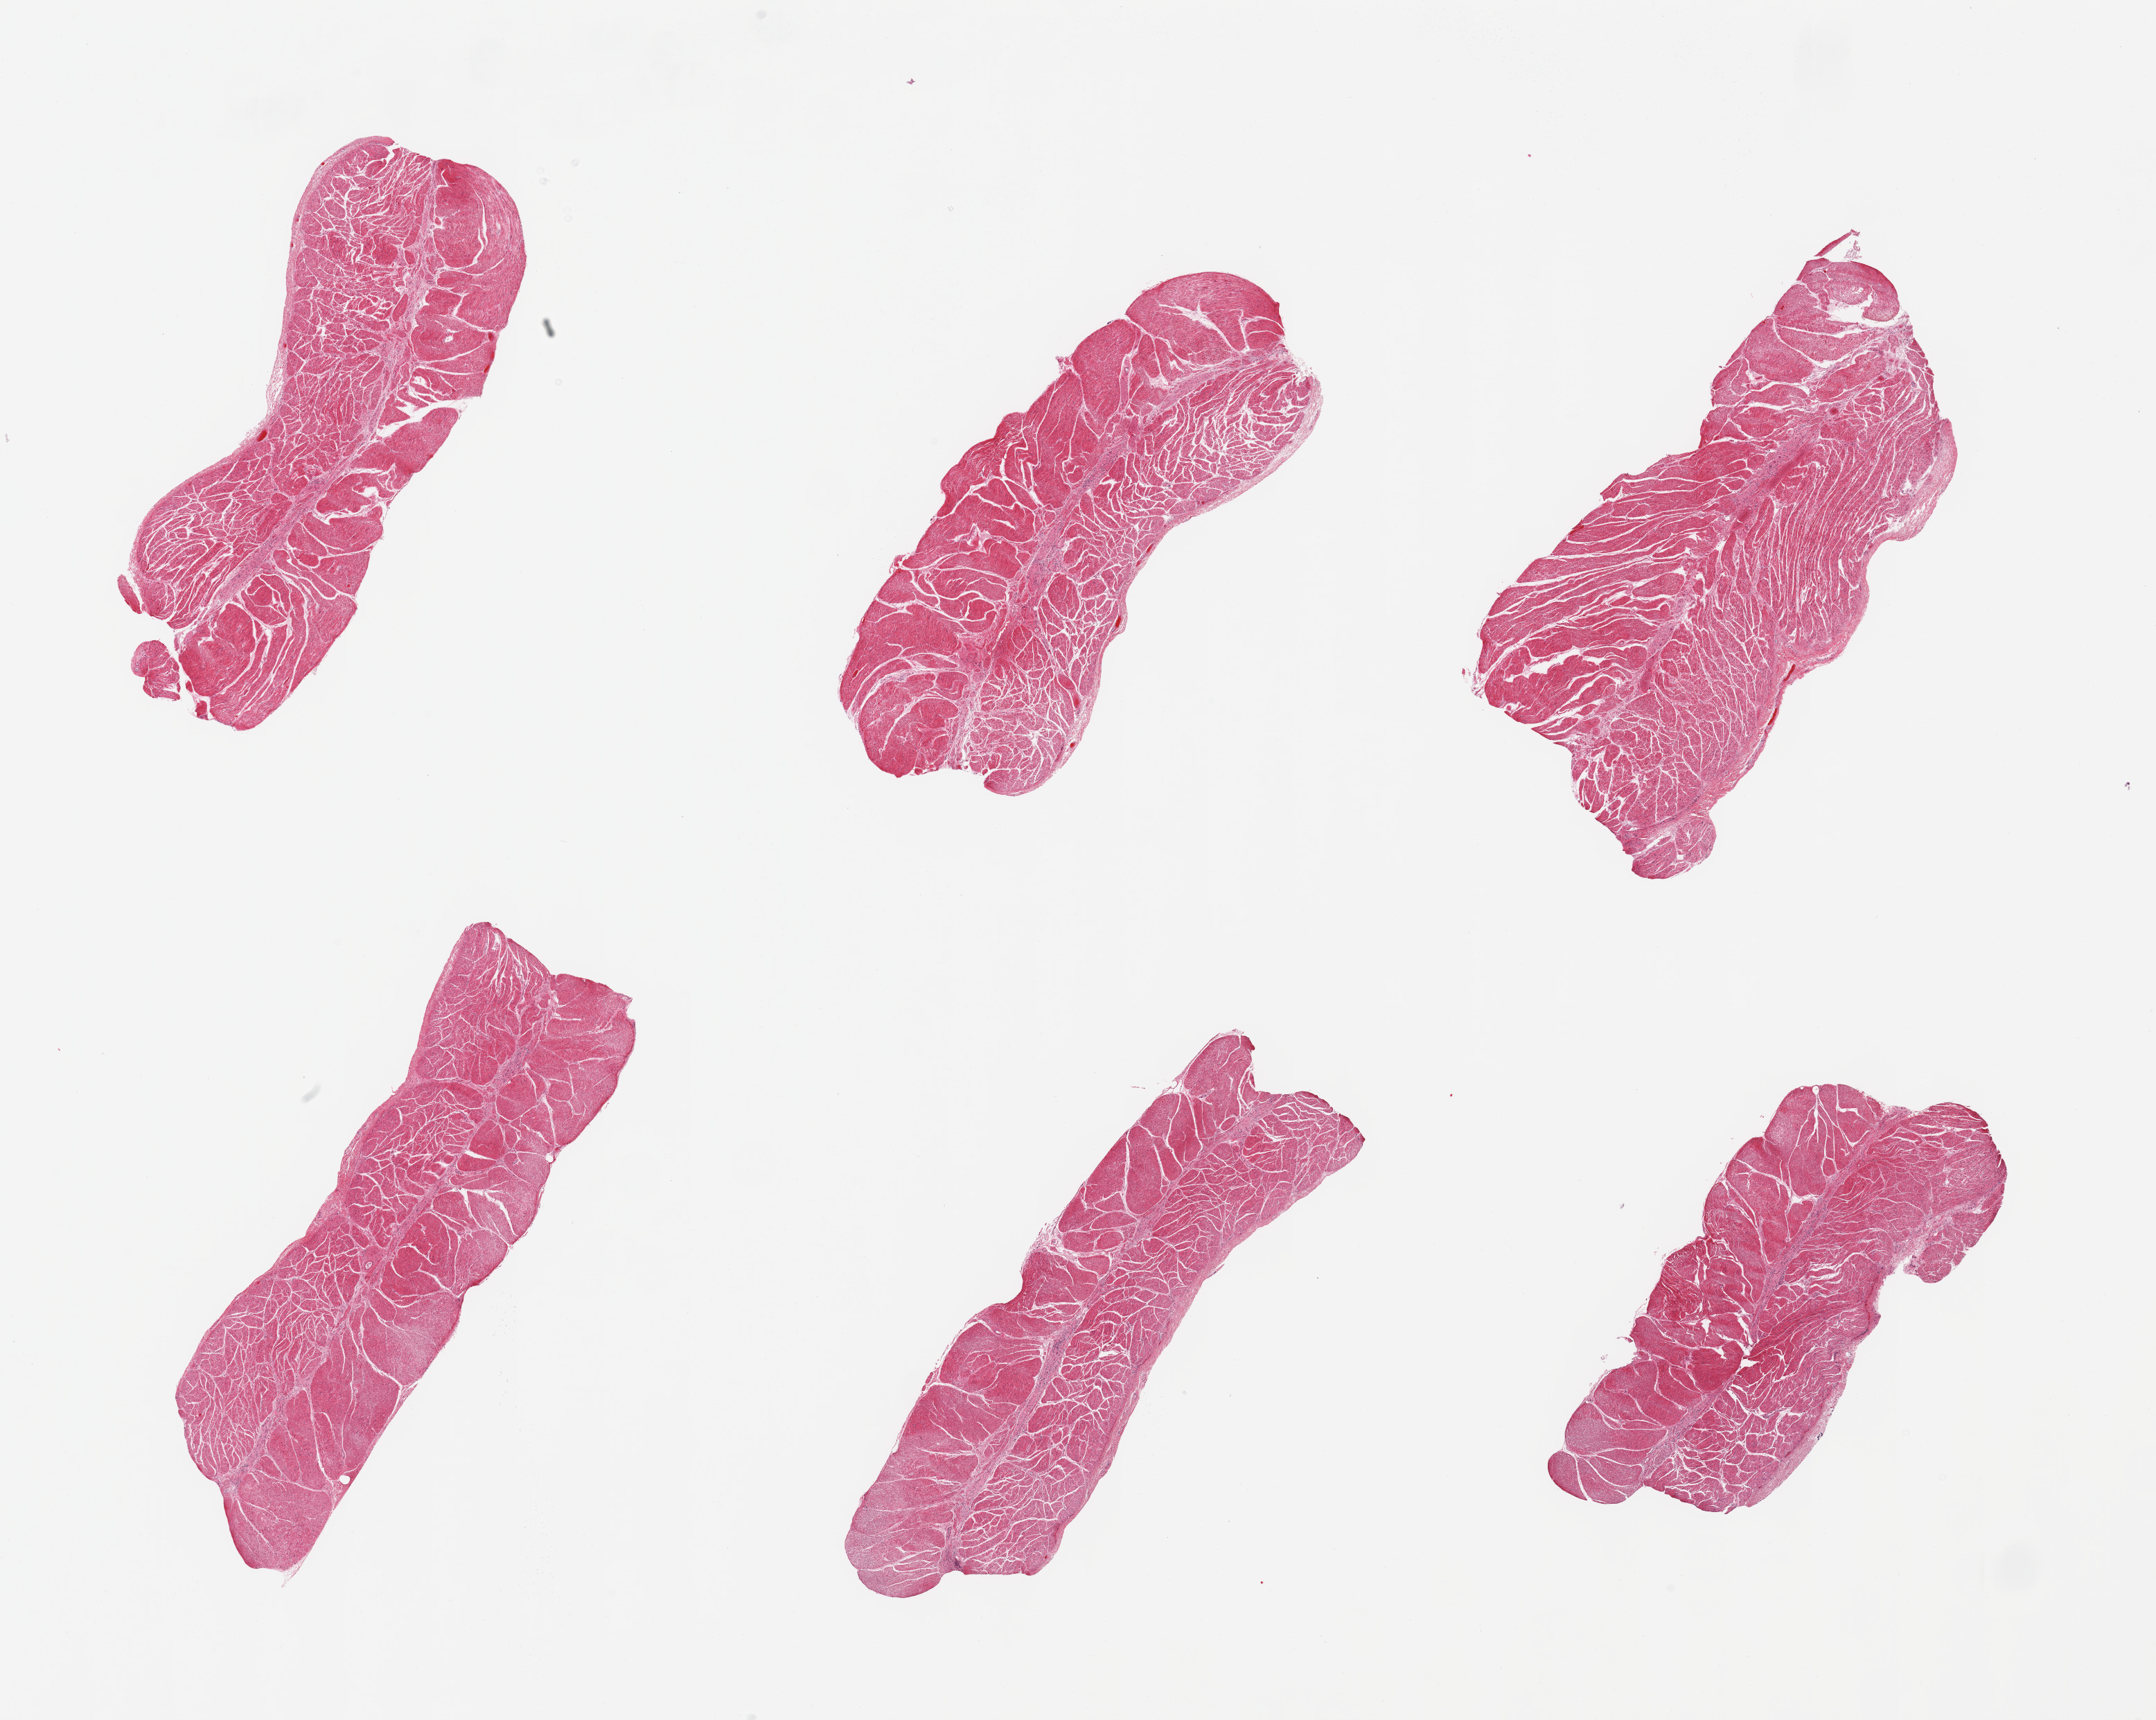
Hematoxylin and eosin (H&E) whole-slide image, brightfield, shown as a low-resolution overview of the whole scanned area (about 24.6 x 19.6 mm, acquisition: 20x scan). PAXgene-fixed paraffin-embedded (PFPE) section. Sampled site (target tissue): esophageal muscle. Donor tissue sample.
• review note (as recorded): 6 pieces; well dissected; not so well preserved